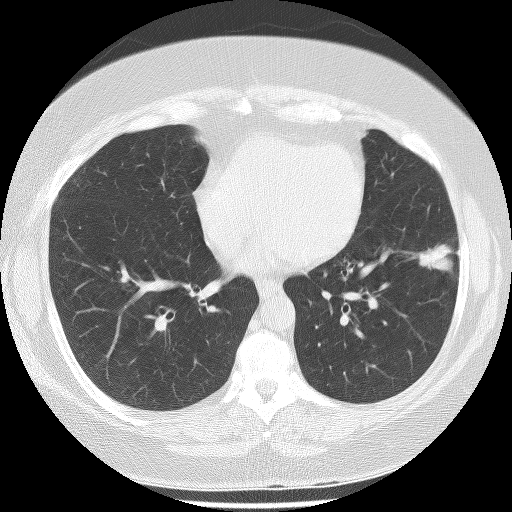
Low-dose screening chest CT, axial slice; baseline annual screen; lung window (W 1500 / L -600 HU); 2.5 mm slice thickness; 512 × 512 image matrix, field of view 340 × 340 mm. Female participant, aged 56 years at enrolment. Former smoker at enrolment.
Expert-annotated lung lesion, bounding box (x1, y1, x2, y2) in pixels: (399, 230, 464, 282). The exam's reader record, not a measurement of the box and not confirmed to be the same lesion: non-calcified nodule or mass ≥4 mm, left lower lobe, 22 × 17 mm, spiculated (stellate) margins, soft tissue attenuation. Later outcome: lung cancer diagnosed 63 days after this screen — bronchiolo-alveolar adenocarcinoma, NOS, left lower lobe, stage IA (AJCC 6th edition), 18 mm at pathology.